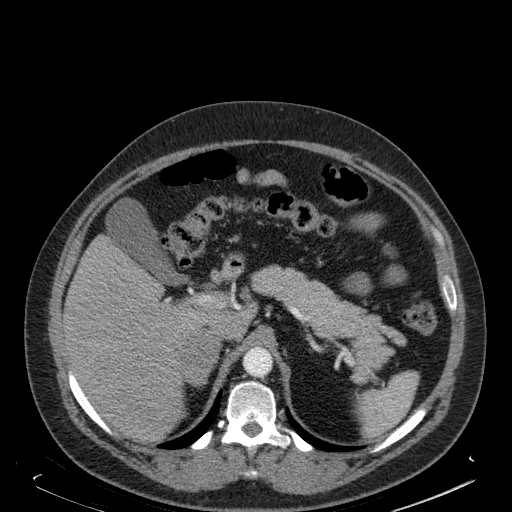
Contrast-enhanced abdominal CT, one axial slice. Position 125 of 181 along the scan axis. Soft-tissue window (W 400 / L 40 HU). 1.5 mm slice thickness. 512 × 512 image matrix, field of view 405 × 405 mm. Male patient. Case-level facts recorded for this patient, not image findings: diagnosis: adrenocortical carcinoma; tumour side: right adrenal; tumour size at pathology: 7.5 cm; Ki-67 index: 25 %; stage (as recorded): 4.
Annotated regions visible in this slice (semi-automatic segmentation, software-assisted and operator-edited):
- mass: bounding box <182,331,217,384> (left, top, right, bottom; pixels)